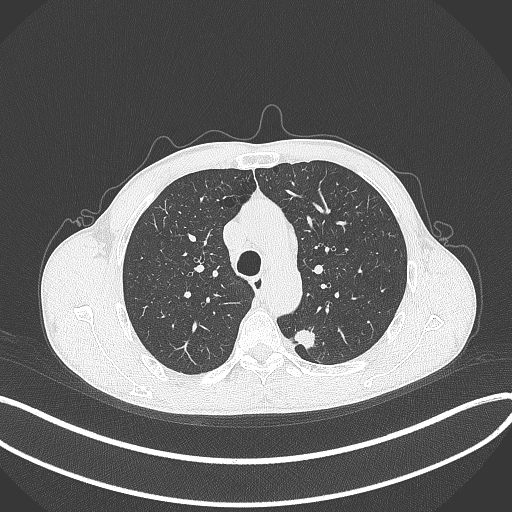
Chest CT, one axial slice. Slice 284 of 429 in the series (ordered by position). Reconstruction kernel B70f. Lung window (W 1500 / L -600 HU). 1 mm slice thickness. 512 × 512 image matrix, field of view 400 × 400 mm. Male patient, age 51 years. From the clinical record (not read from this slice): clinical TNM (as recorded): T2a N1 M1.
Annotated regions visible in this slice (bounding box drawn by a radiologist):
- lung tumour (recorded histology: adenocarcinoma): bounding box (x1, y1, x2, y2) in pixels: (290, 325, 319, 352)